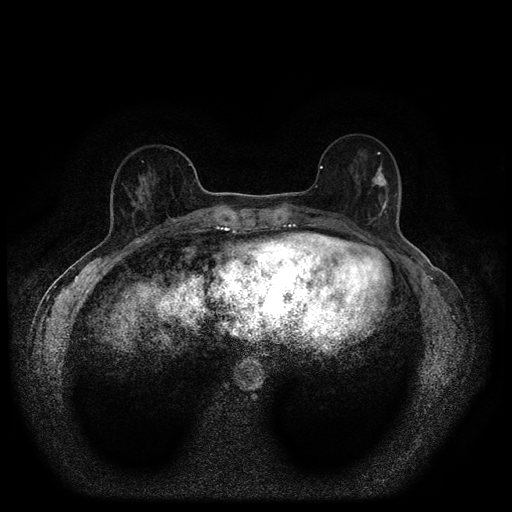
Breast MRI (dynamic contrast-enhanced, multi-phase), one axial slice; slice 35 of 116 in the series (ordered by position); dynamic contrast-enhanced series, time point 2 of 5 at this slice position (early post-contrast); 1.5 T; TE 2.7 ms, TR 5.4 ms; 512 × 512 image matrix, field of view 330 × 330 mm. Patient: female, 56 years.
Structures marked on this image (semi-automatic segmentation, software-assisted and operator-edited):
- breast lesion (labelled 'tumour' in the annotation; benign lesions carry a separate 'benign' label): bounding box <371,159,388,217> (left, top, right, bottom; pixels)